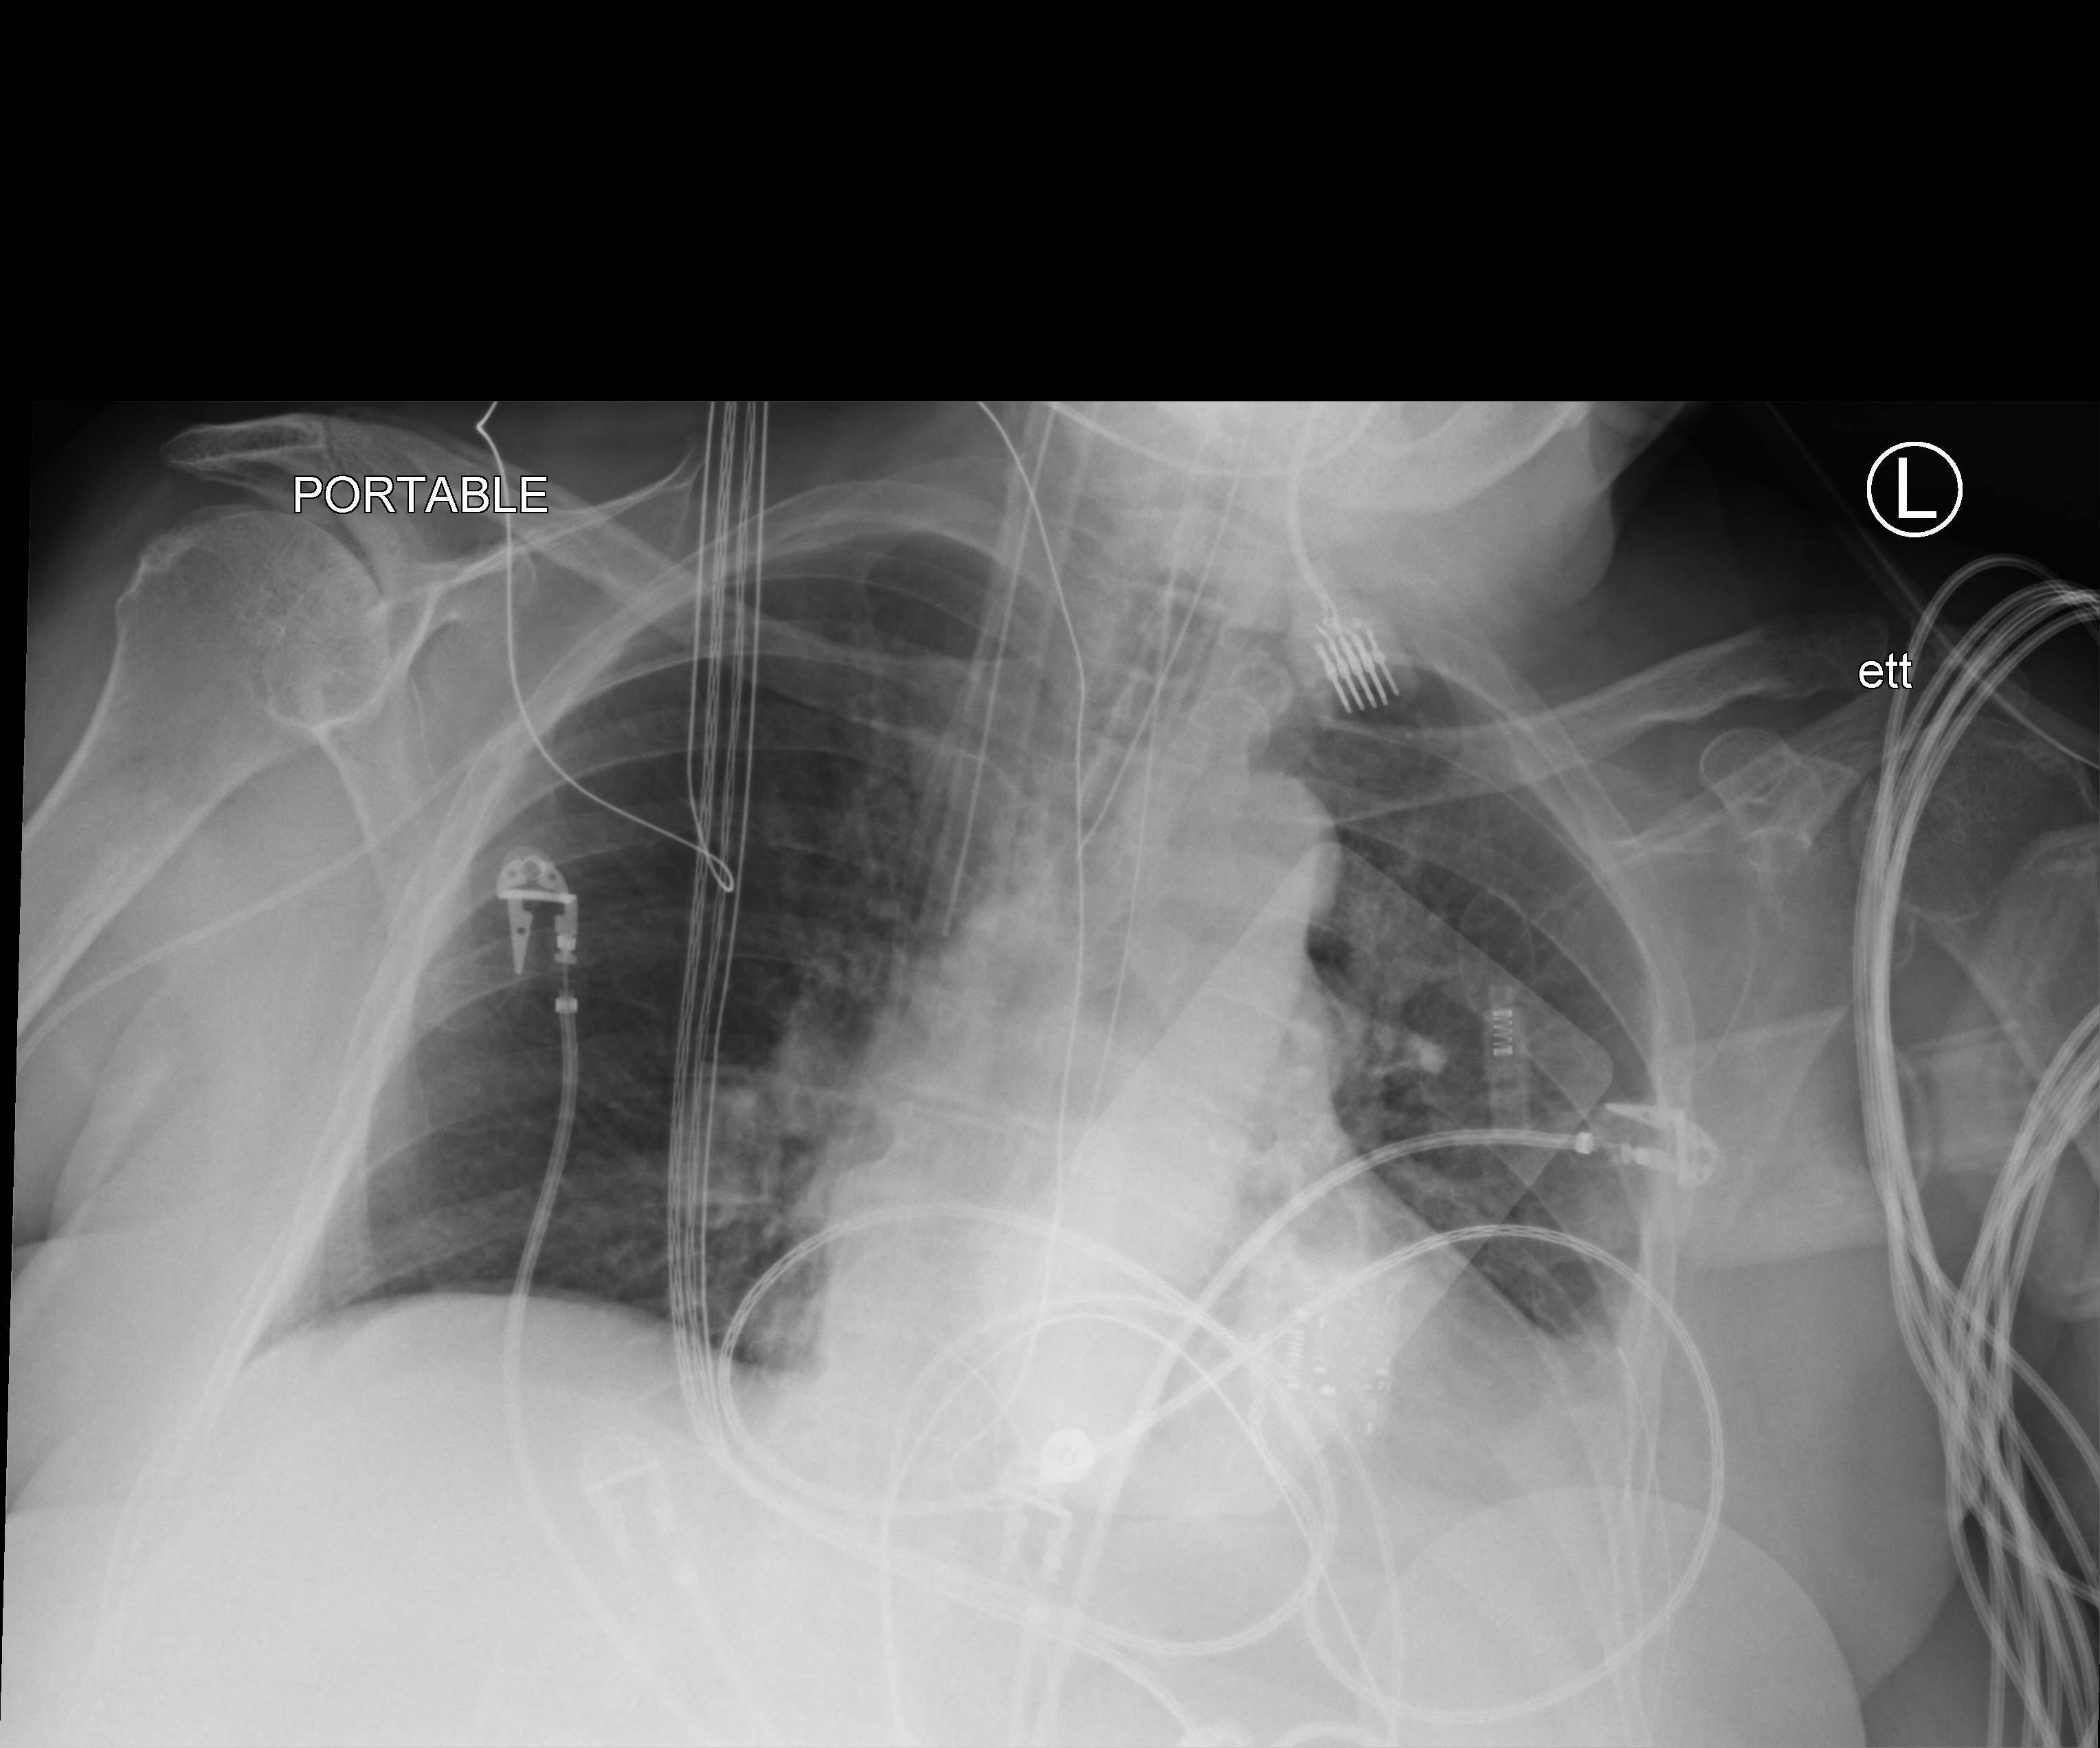
Chest X-ray (portable). Patient hospitalised with COVID-19; female, aged 75–90 years.
From the hospital-stay record, not from the radiograph (when in the stay this image was taken is not recorded): admitted to intensive care during this hospital stay: yes.